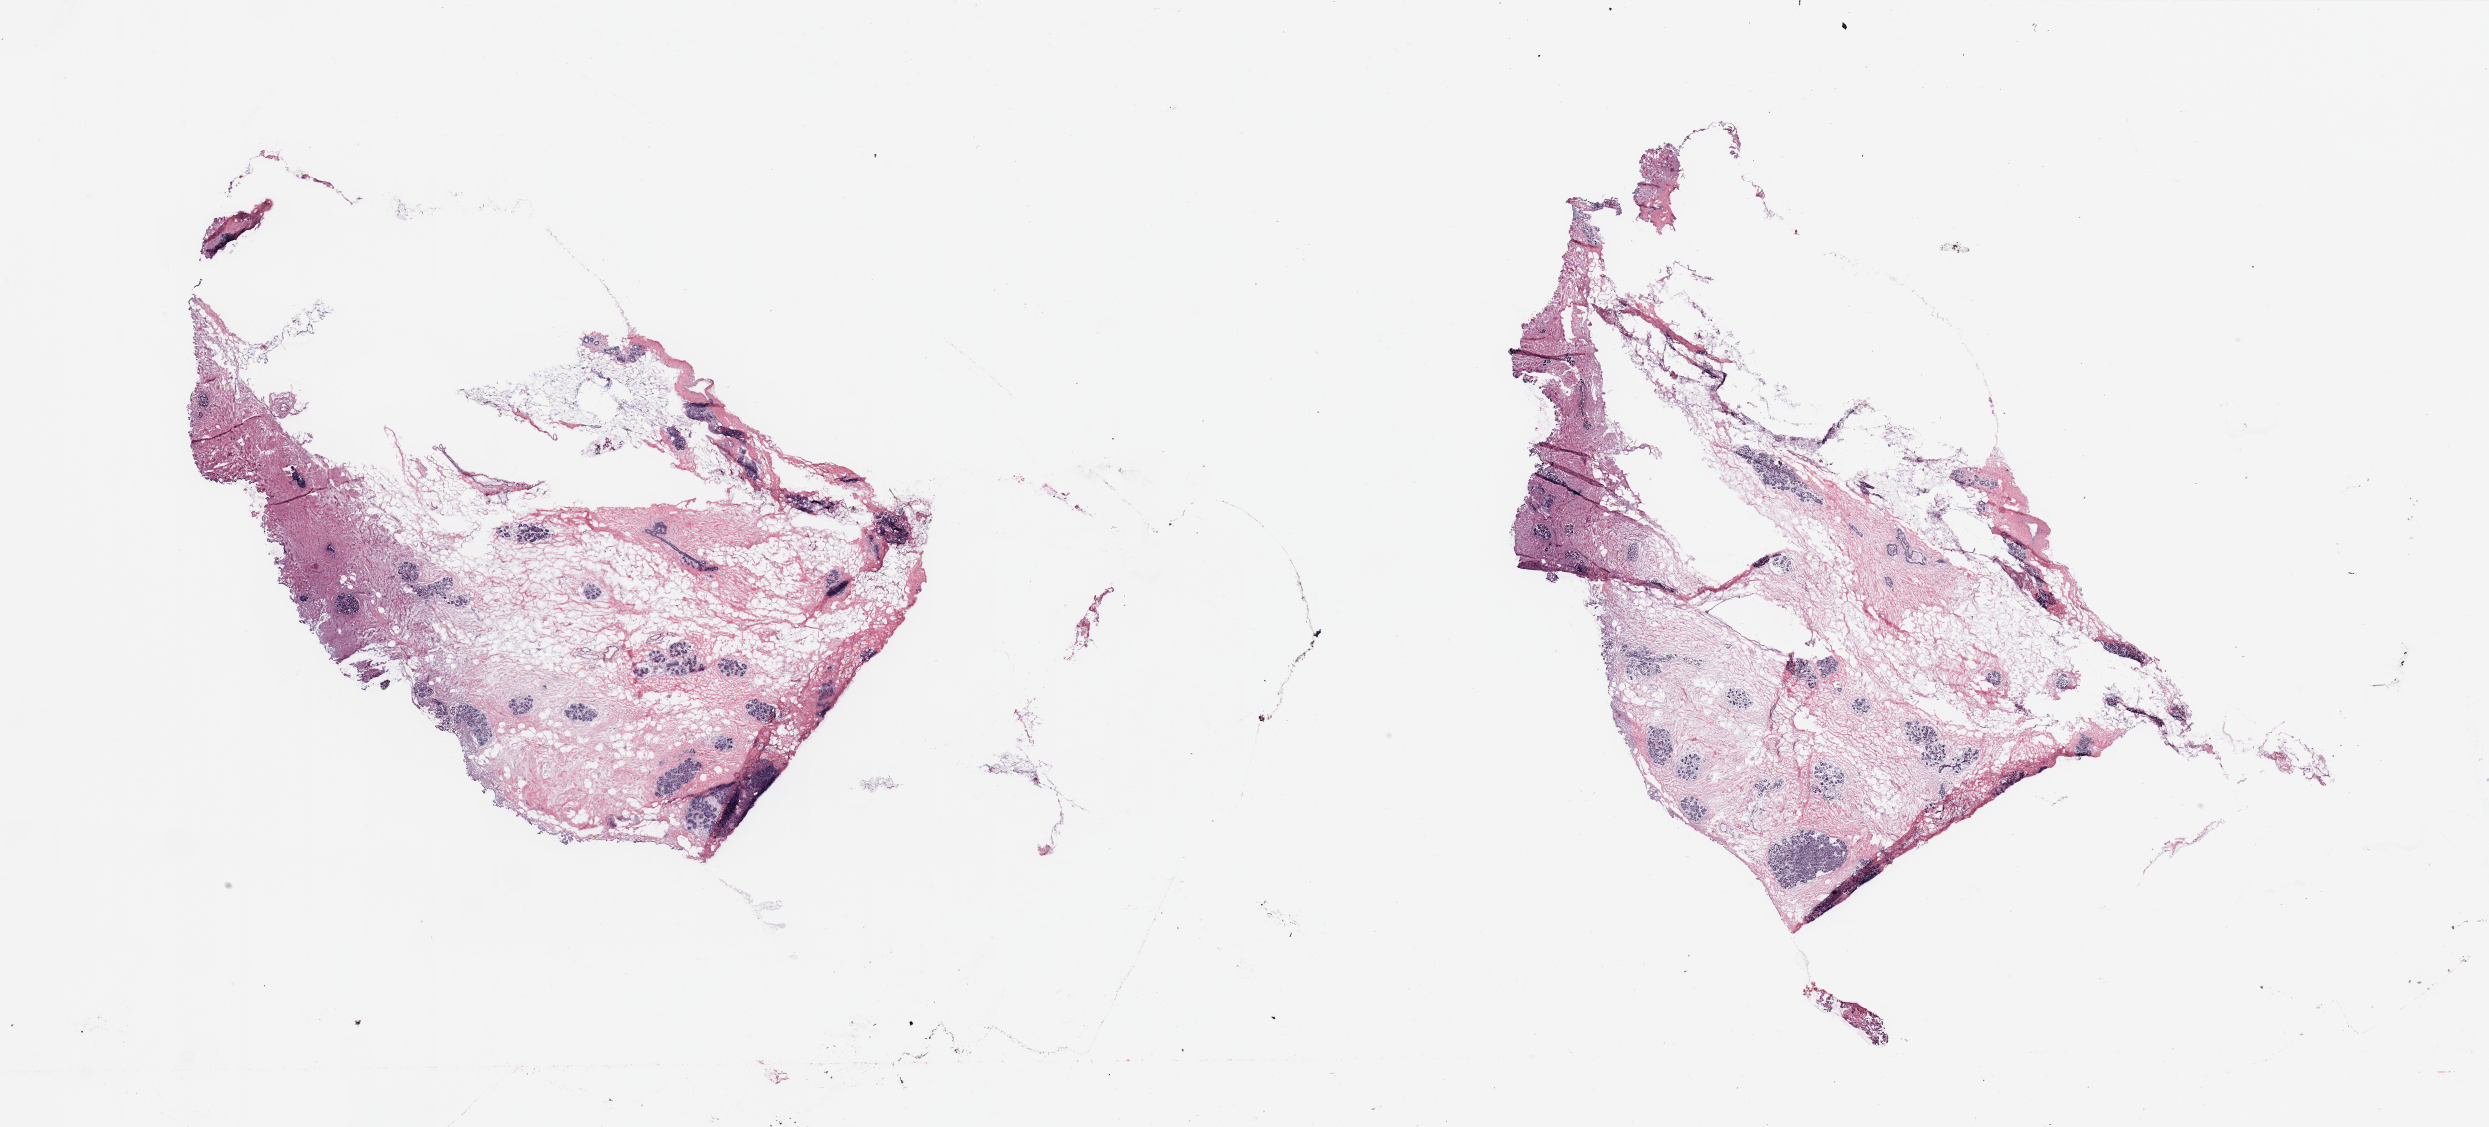
Hematoxylin and eosin (H&E) stained whole-slide image, low-resolution overview of the scanned area, about 39.4 x 17.8 mm (acquisition: 20x scan), tumour tissue sample, breast. Female, 37 y/o.
Diagnosis: Infiltrating duct carcinoma, NOS.